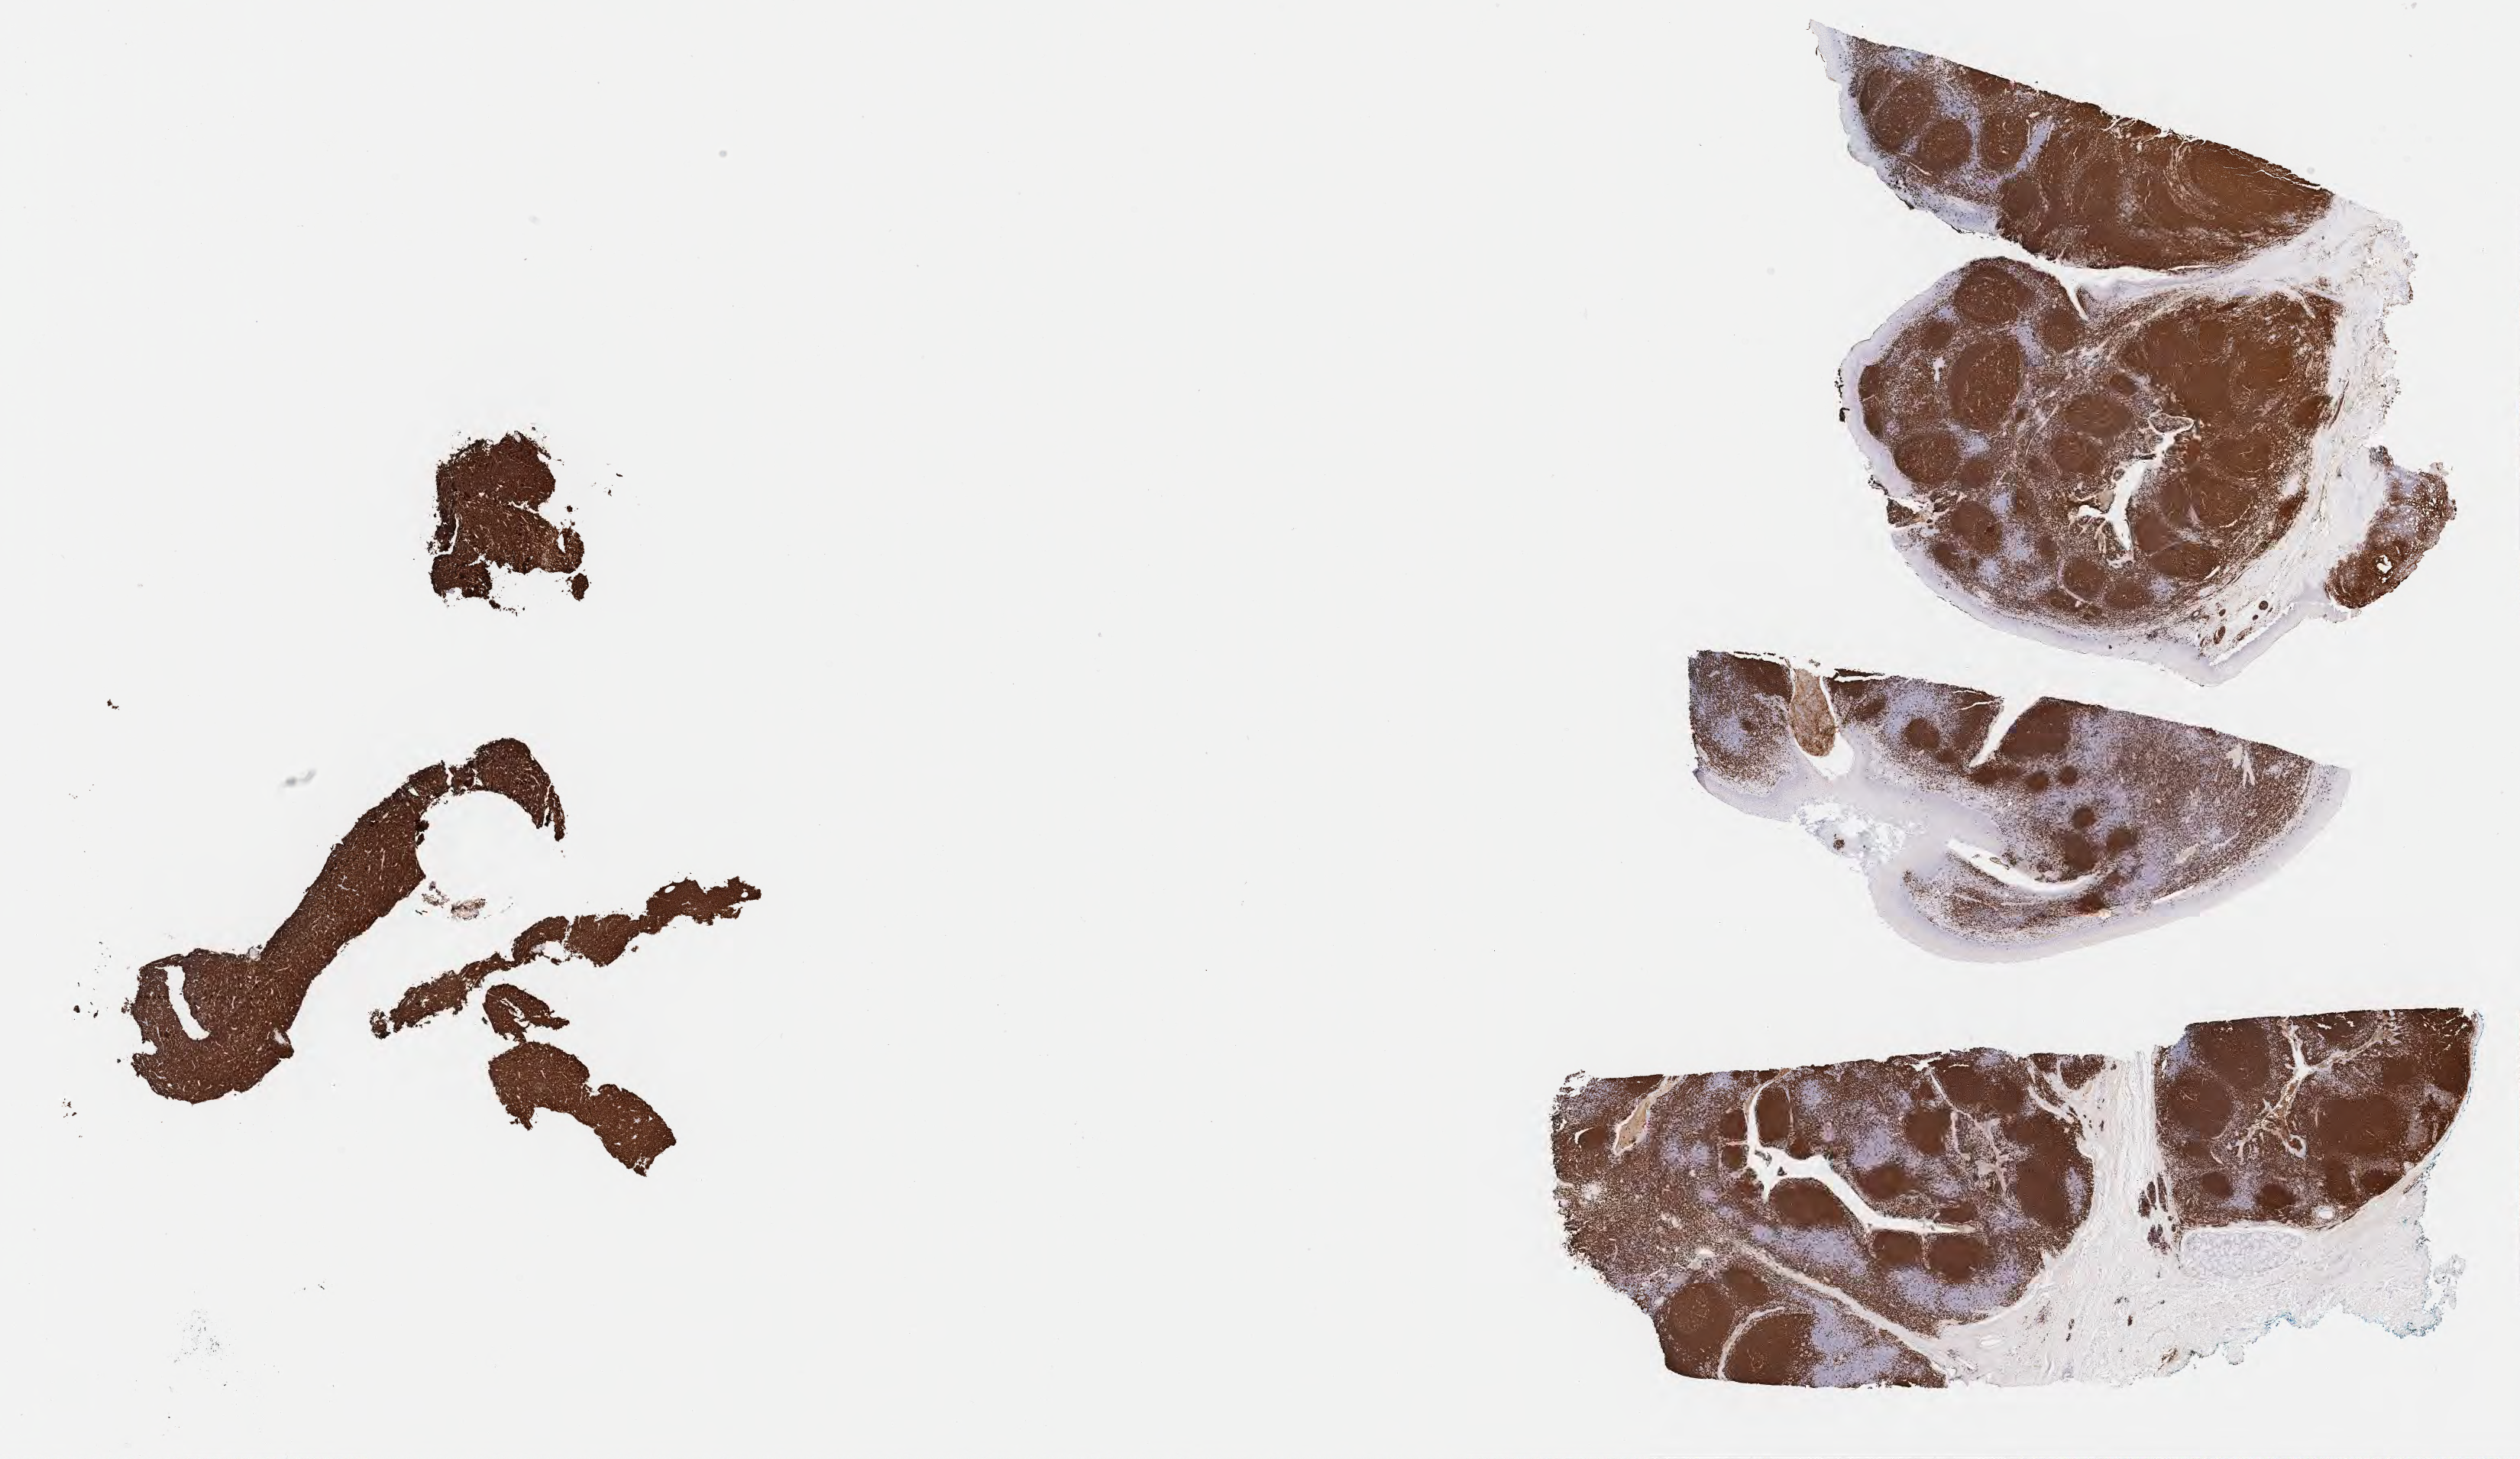
Immunohistochemistry (IHC) whole-slide image stained for CD20 — a low-resolution overview of the entire scanned area, about 26.7 x 15.4 mm; tumor tissue; site: cranium. Male patient; age at initial diagnosis 5 years.
- histologic diagnosis: Burkitt lymphoma, NOS